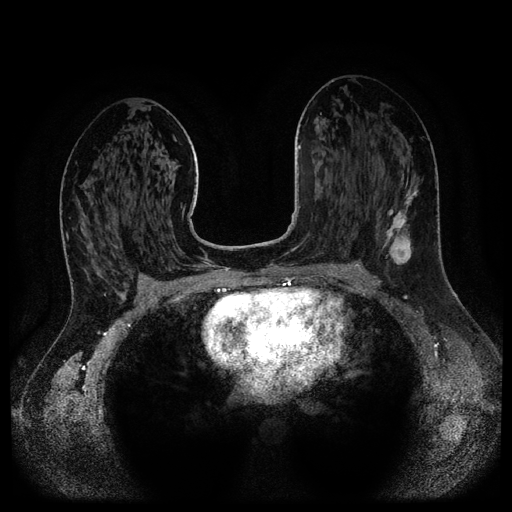
Breast MRI (dynamic contrast-enhanced, multi-phase), one axial slice; slice 60 of 116 in the series (ordered by position); dynamic contrast-enhanced series, time point 2 of 5 at this slice position (early post-contrast); 1.5 T; TE 2.6 ms, TR 5.3 ms; 2.1 mm slice thickness; 512 × 512 image matrix. Female patient, age 37 years.
Outlined on this slice (semi-automatically segmented with operator editing):
- breast lesion (labelled 'tumour' in the annotation; benign lesions carry a separate 'benign' label): bounding box <382,189,418,268> (left, top, right, bottom; pixels)